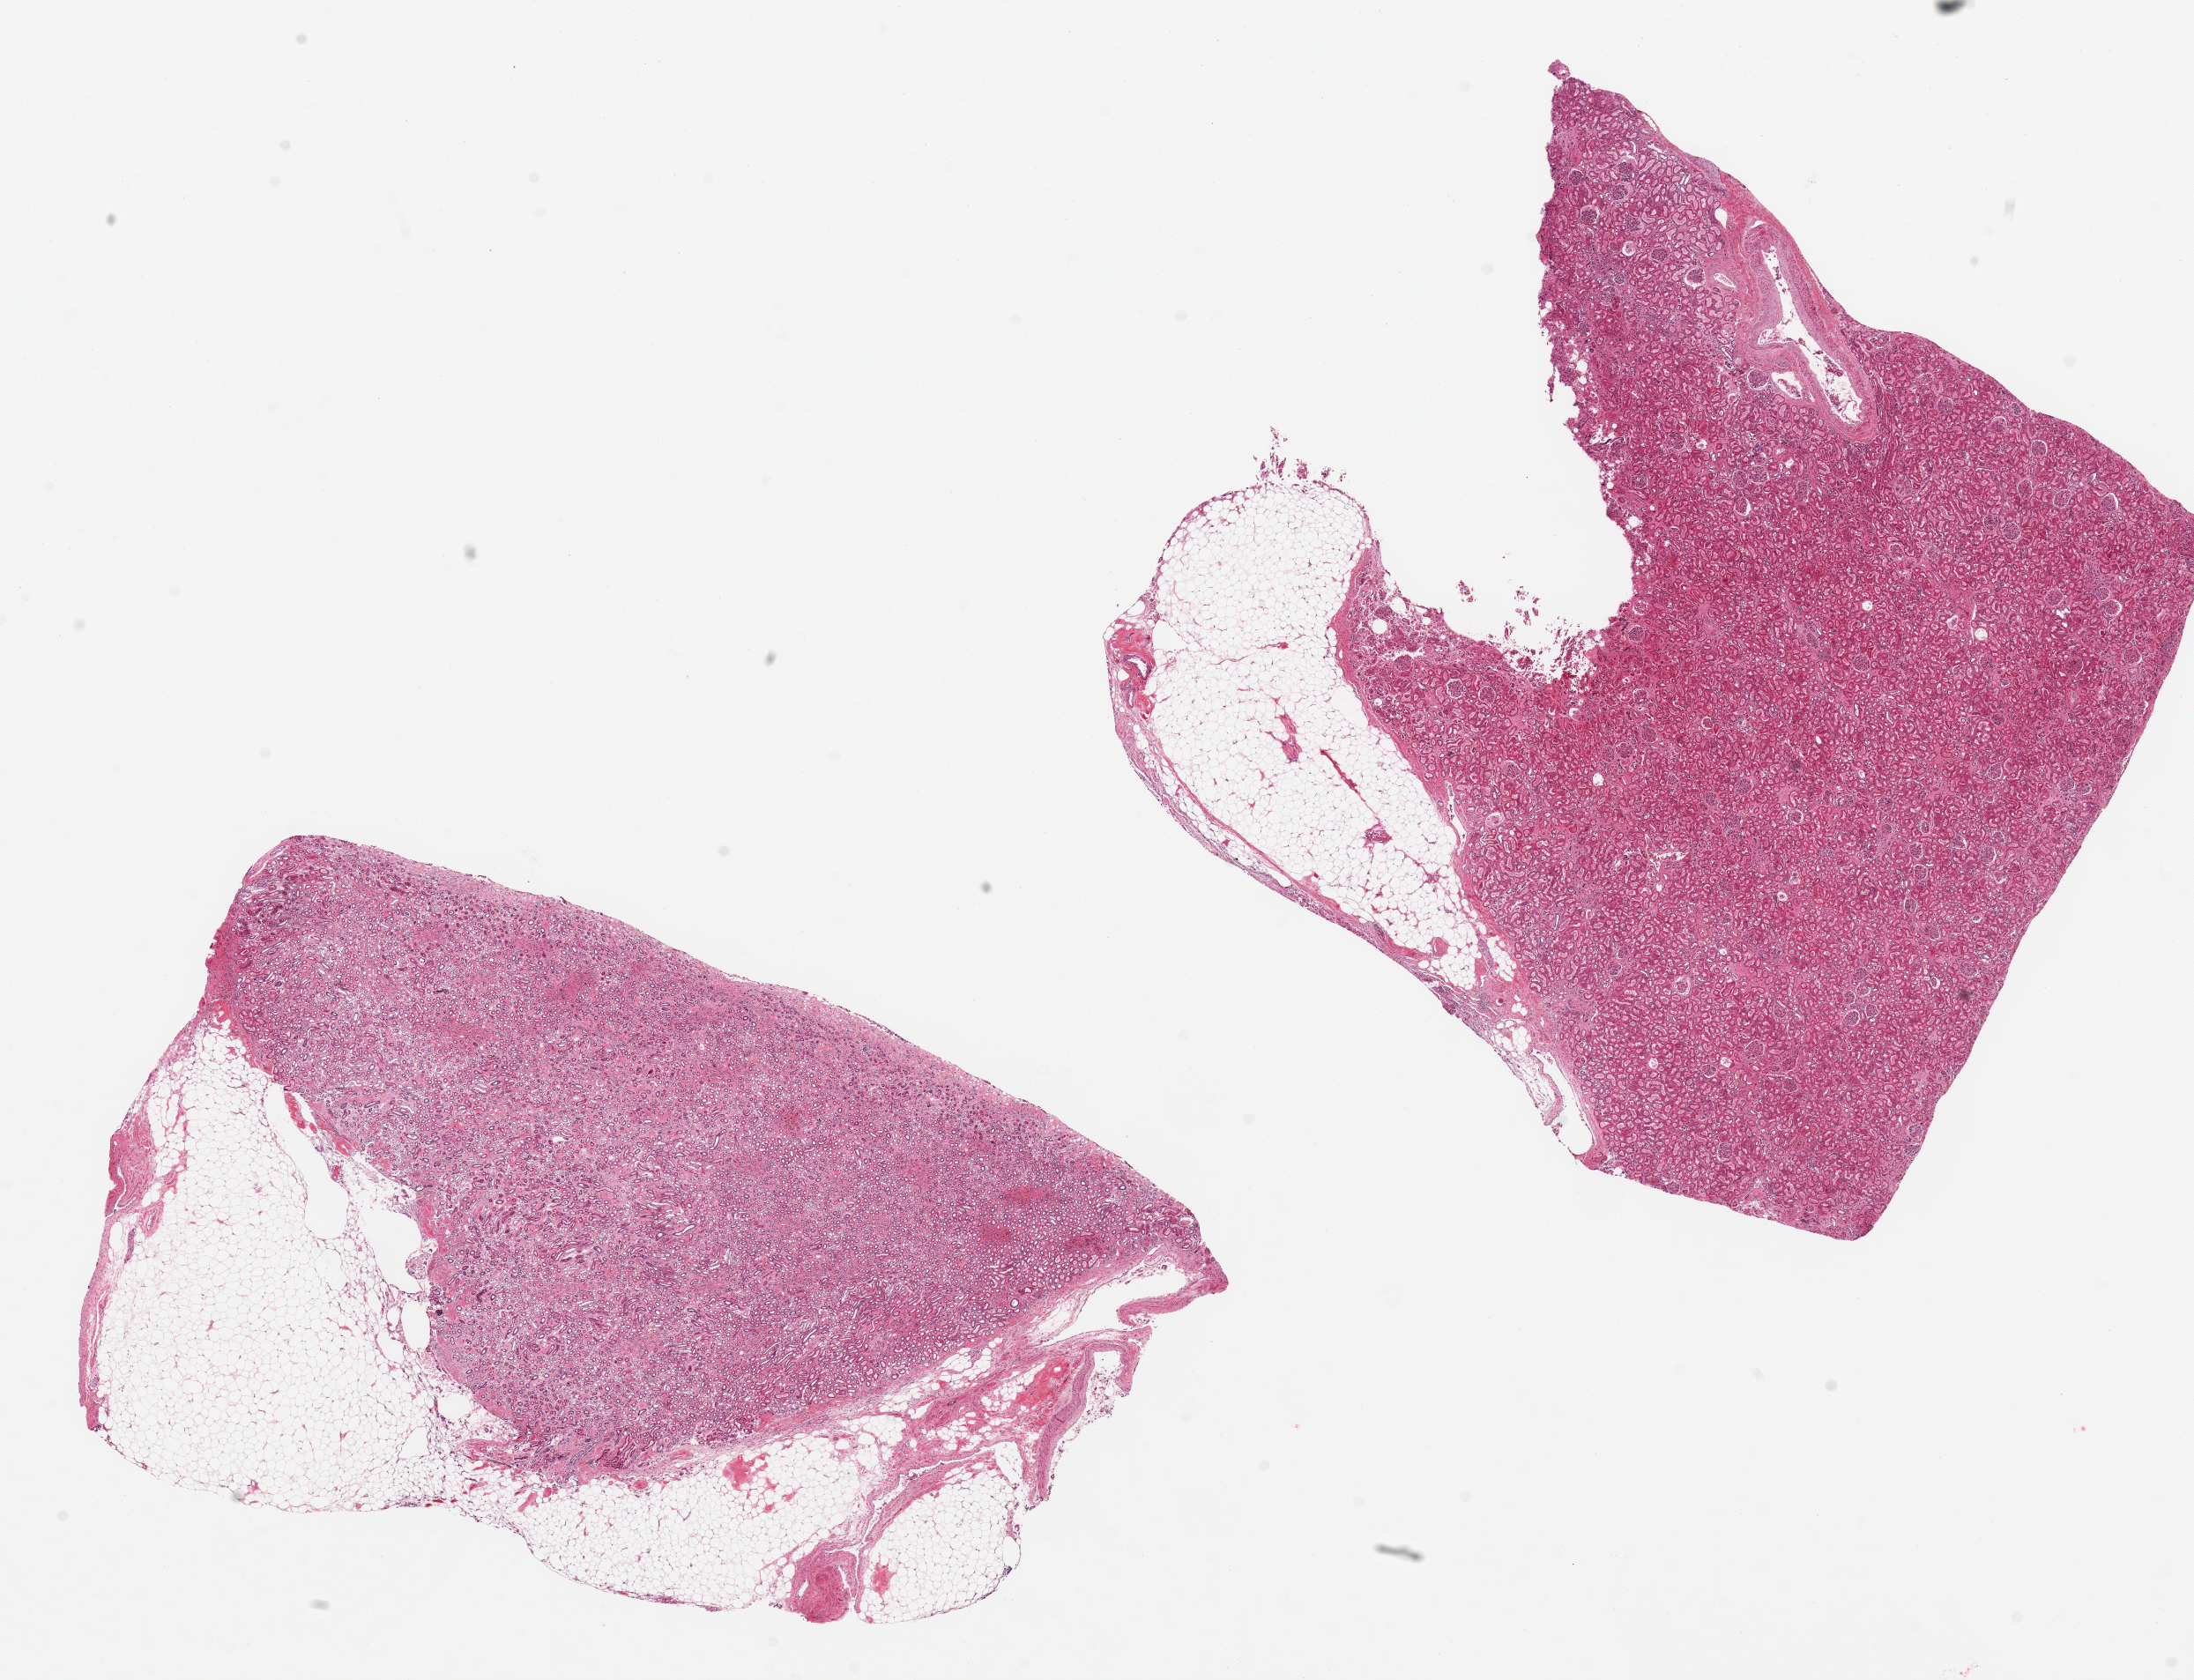
Digitized hematoxylin and eosin (H&E)-stained section, a low-resolution overview of the entire scanned area, about 19.7 x 15.1 mm (slide scanned at 20x). PAXgene-fixed paraffin-embedded (PFPE) section. Target tissue: renal medulla. Donor tissue sample. Male donor.
Pathologist's review note for this sample: 2 pieces: 8.7x5 mm medulla; 8x7 mm cortex; 20-40% adipose.